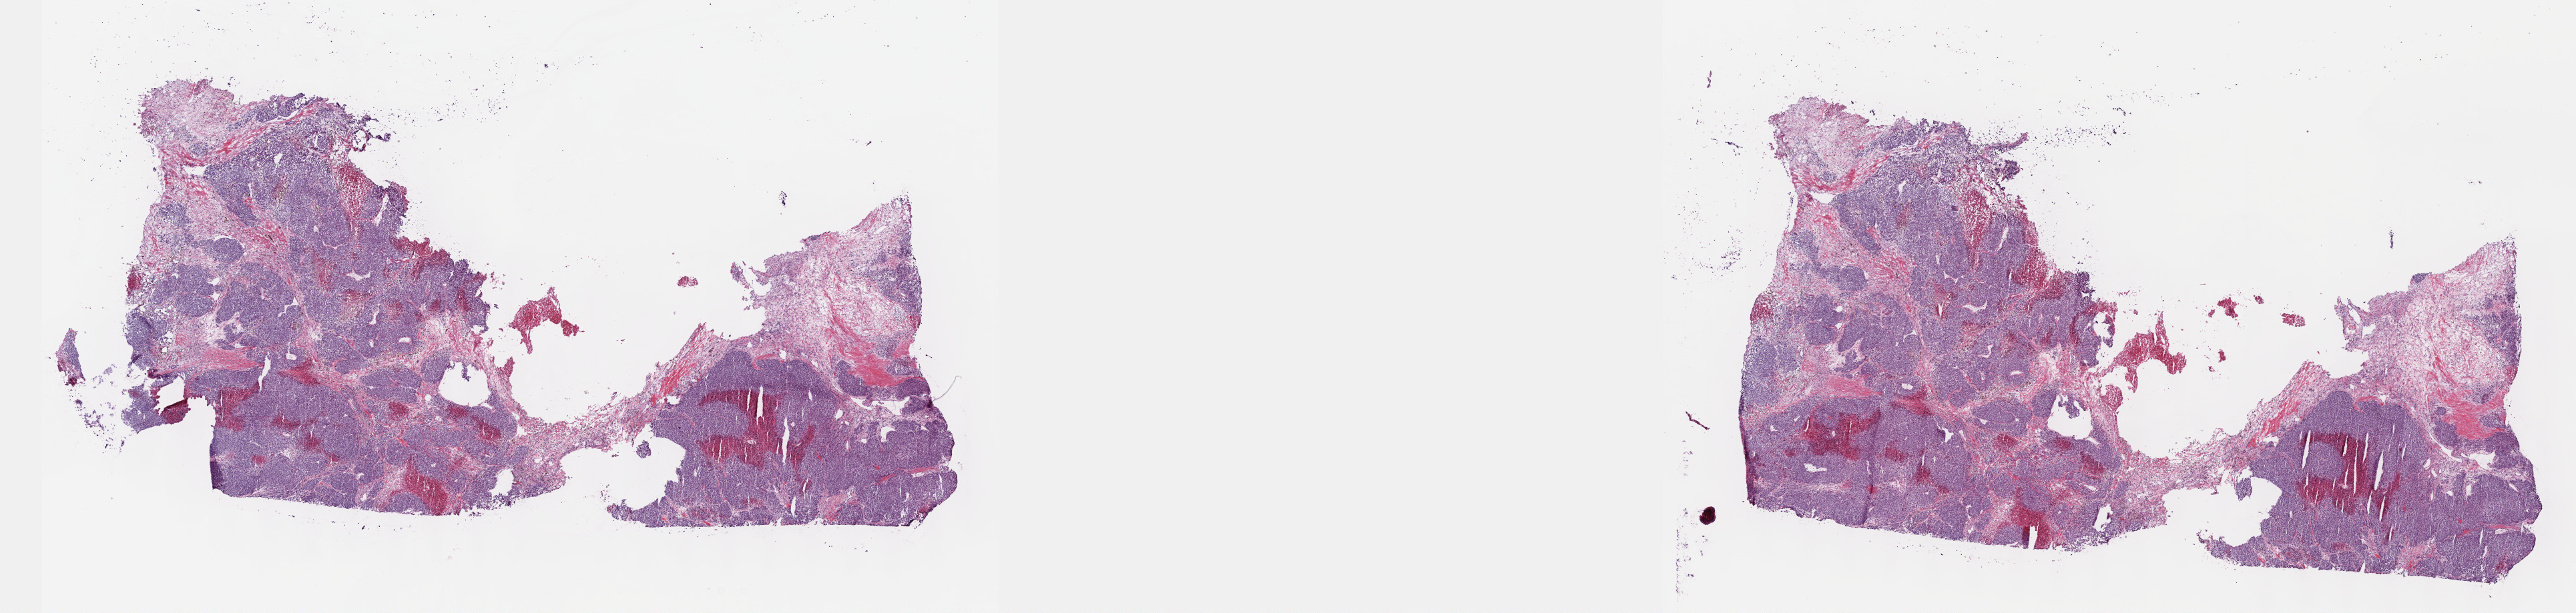
Digitized Hematoxylin and eosin (H&E) stained tissue section (whole slide), shown as a low-resolution overview of the whole scanned area (about 31.2 x 7.4 mm), frozen section from the top of the tissue portion, metastatic tumour sample, sampled site not recorded. Male, age 50 years at initial diagnosis. Slide review estimates, as recorded: tumour cells 60%, tumour nuclei 70%, normal cells 20%, stromal cells 10%, necrosis 10%. Inflammatory infiltration, as recorded: lymphocyte infiltration 0%, monocyte infiltration 0%, neutrophil infiltration 0%.
This section: metastatic tumour tissue. Patient diagnosis: Malignant melanoma, NOS.